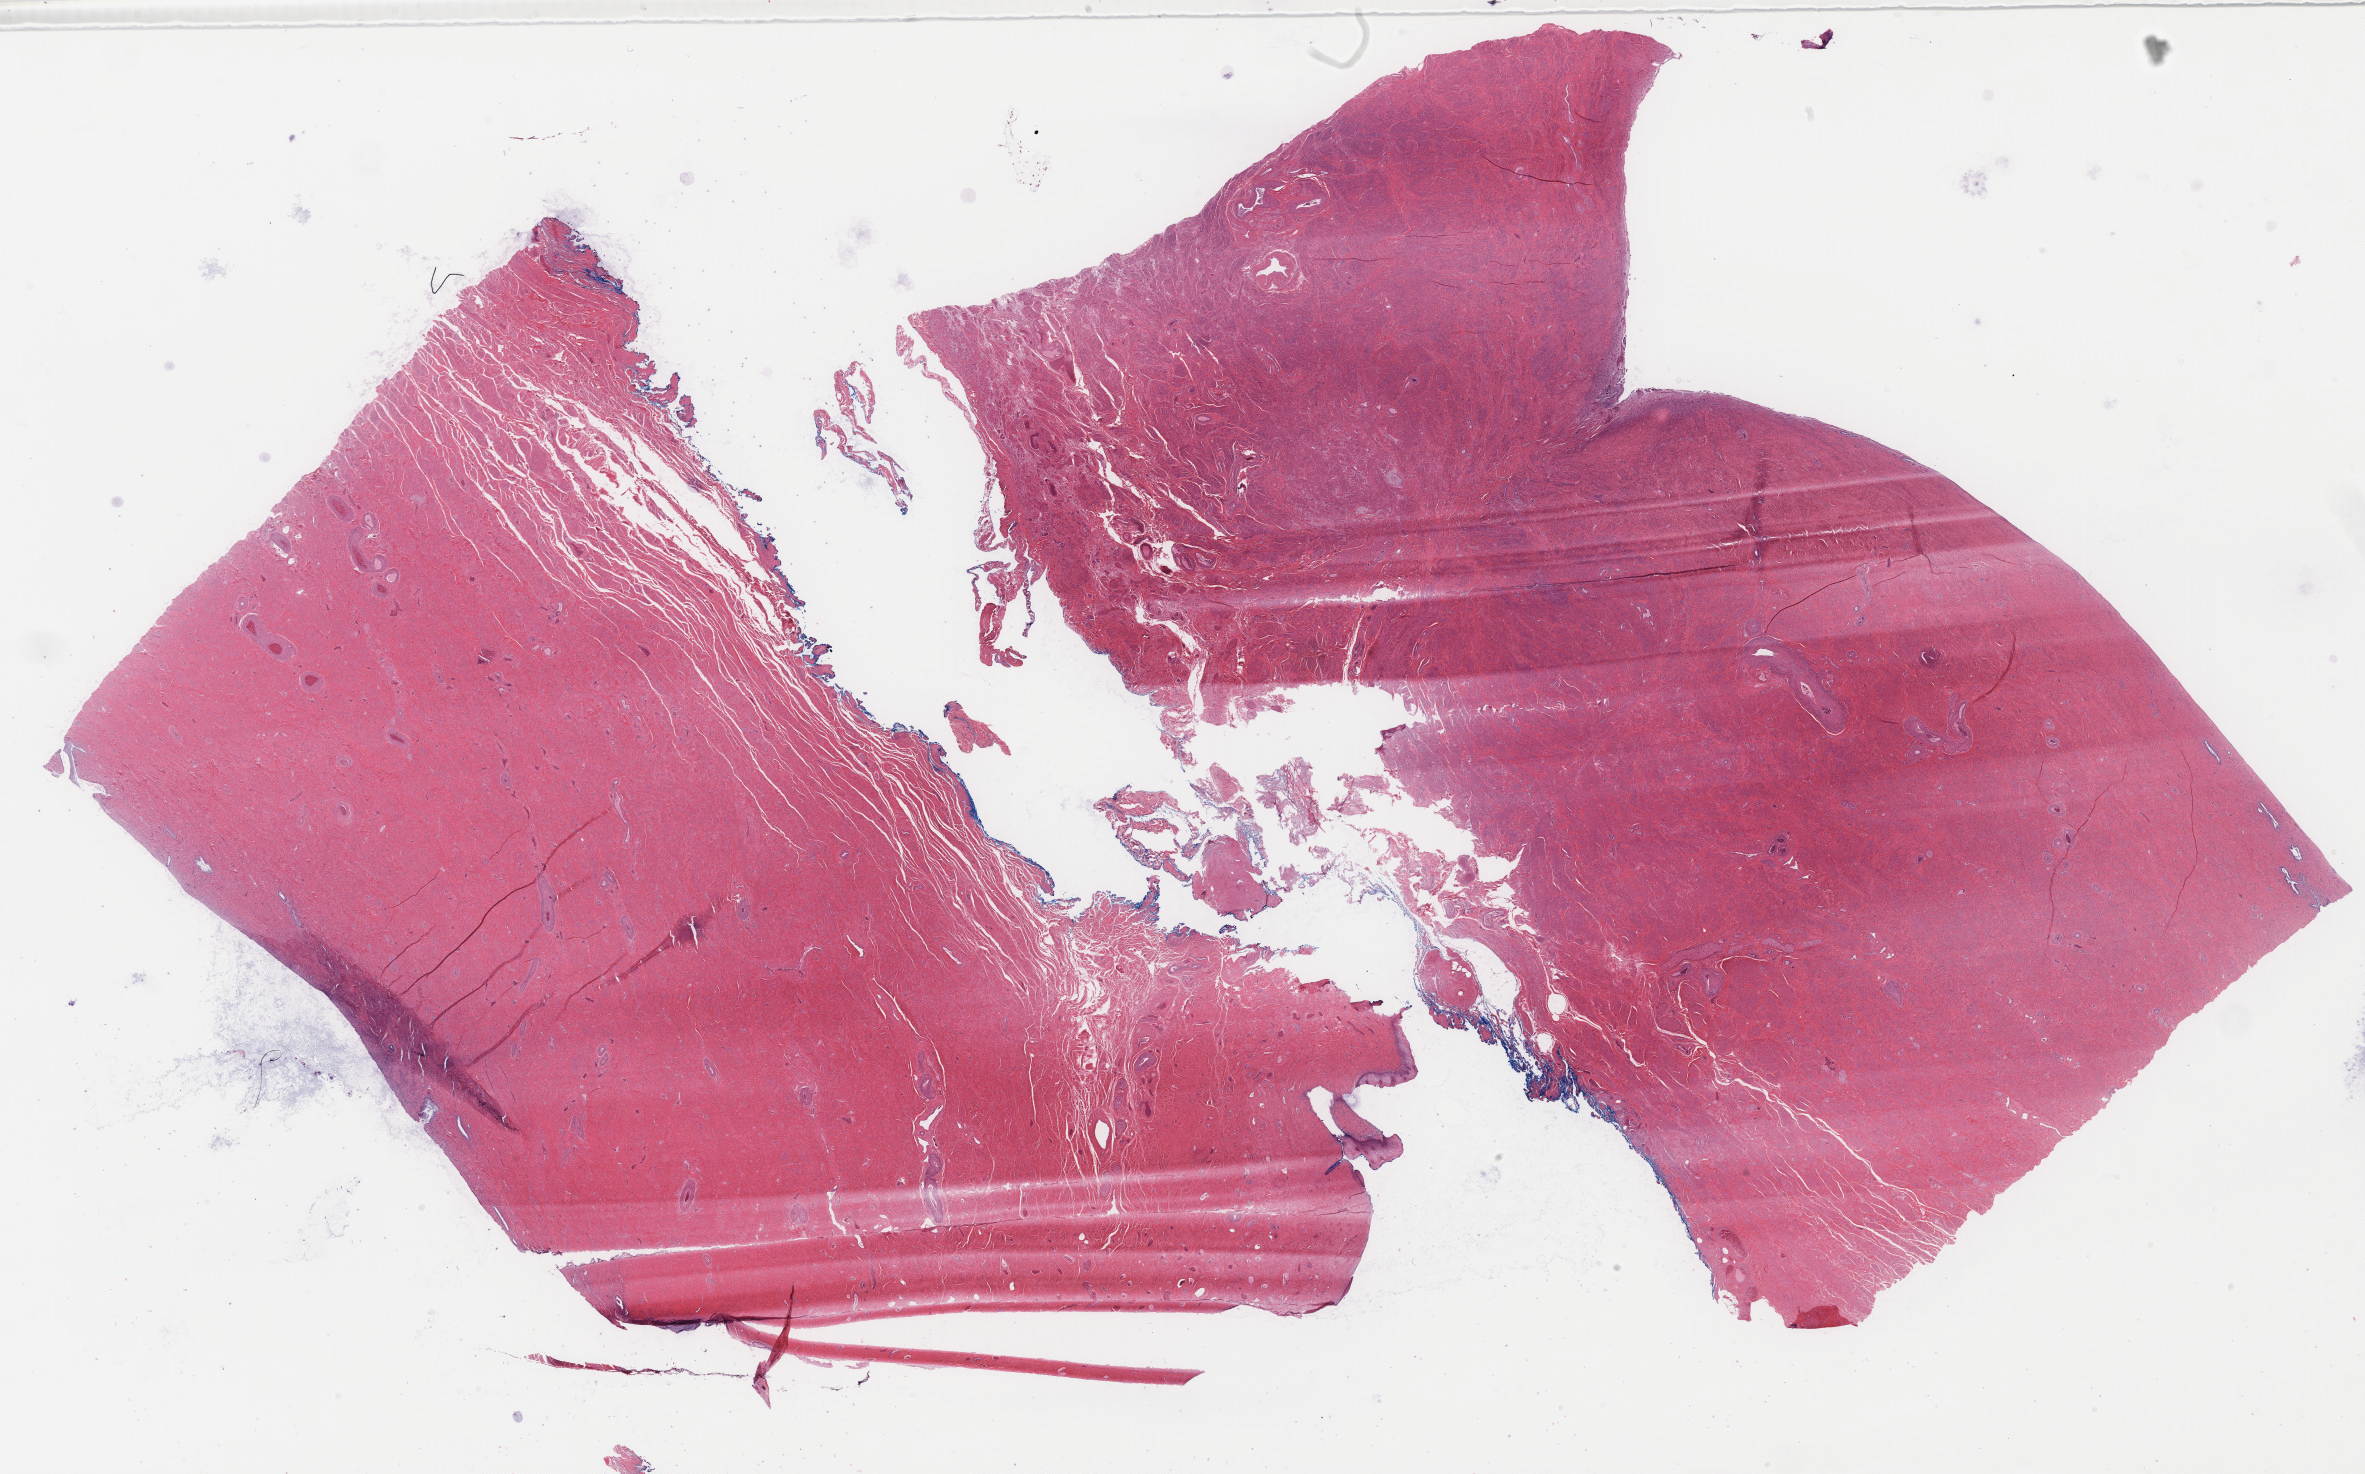
Hematoxylin and eosin (H&E) whole-slide image — low-resolution overview of the scanned area, about 37.4 x 23.3 mm; frozen section; specimen: non-tumor (normal tissue) sample from a patient with serous carcinoma, NOS; anatomic site: body of uterus. Female patient.
This section: non-tumor tissue sample; the patient's diagnosis is given above.